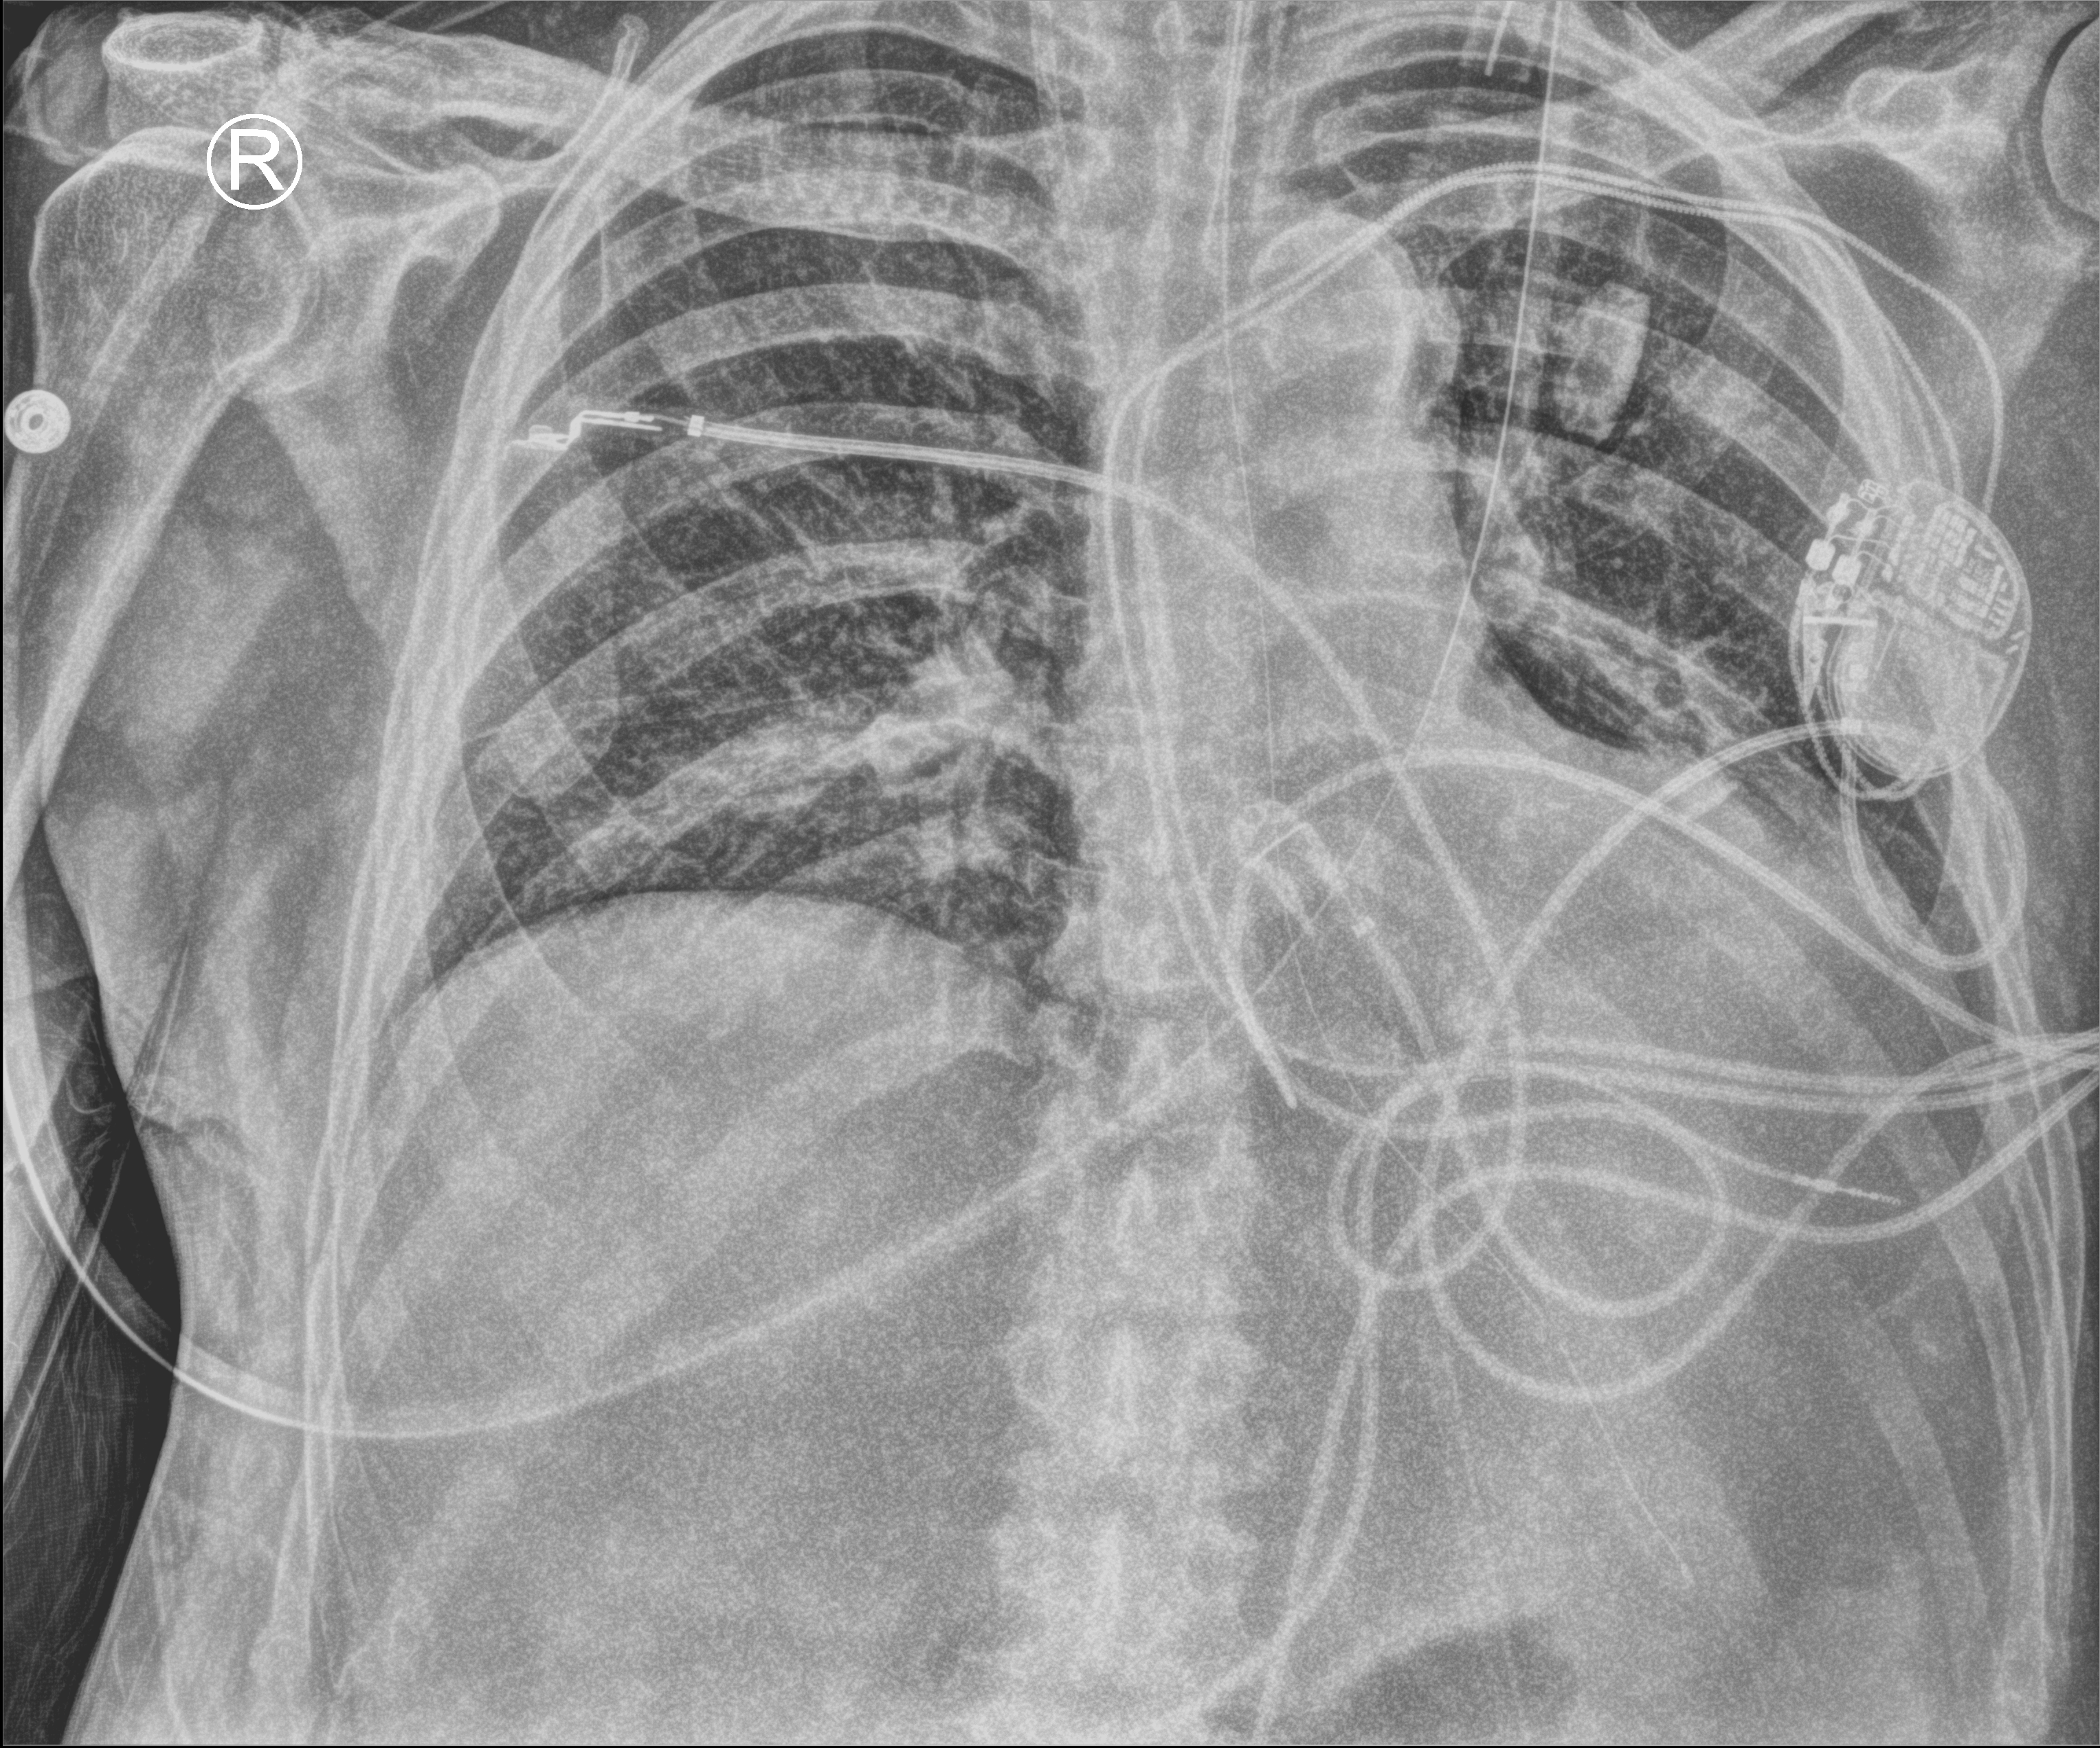
Portable chest radiograph, anteroposterior (AP) projection. Male patient hospitalised with COVID-19, age 60–74 years.
Hospital-stay facts (about this admission, not read from this image; timing relative to this image not recorded): admitted to intensive care during this hospital stay: yes.